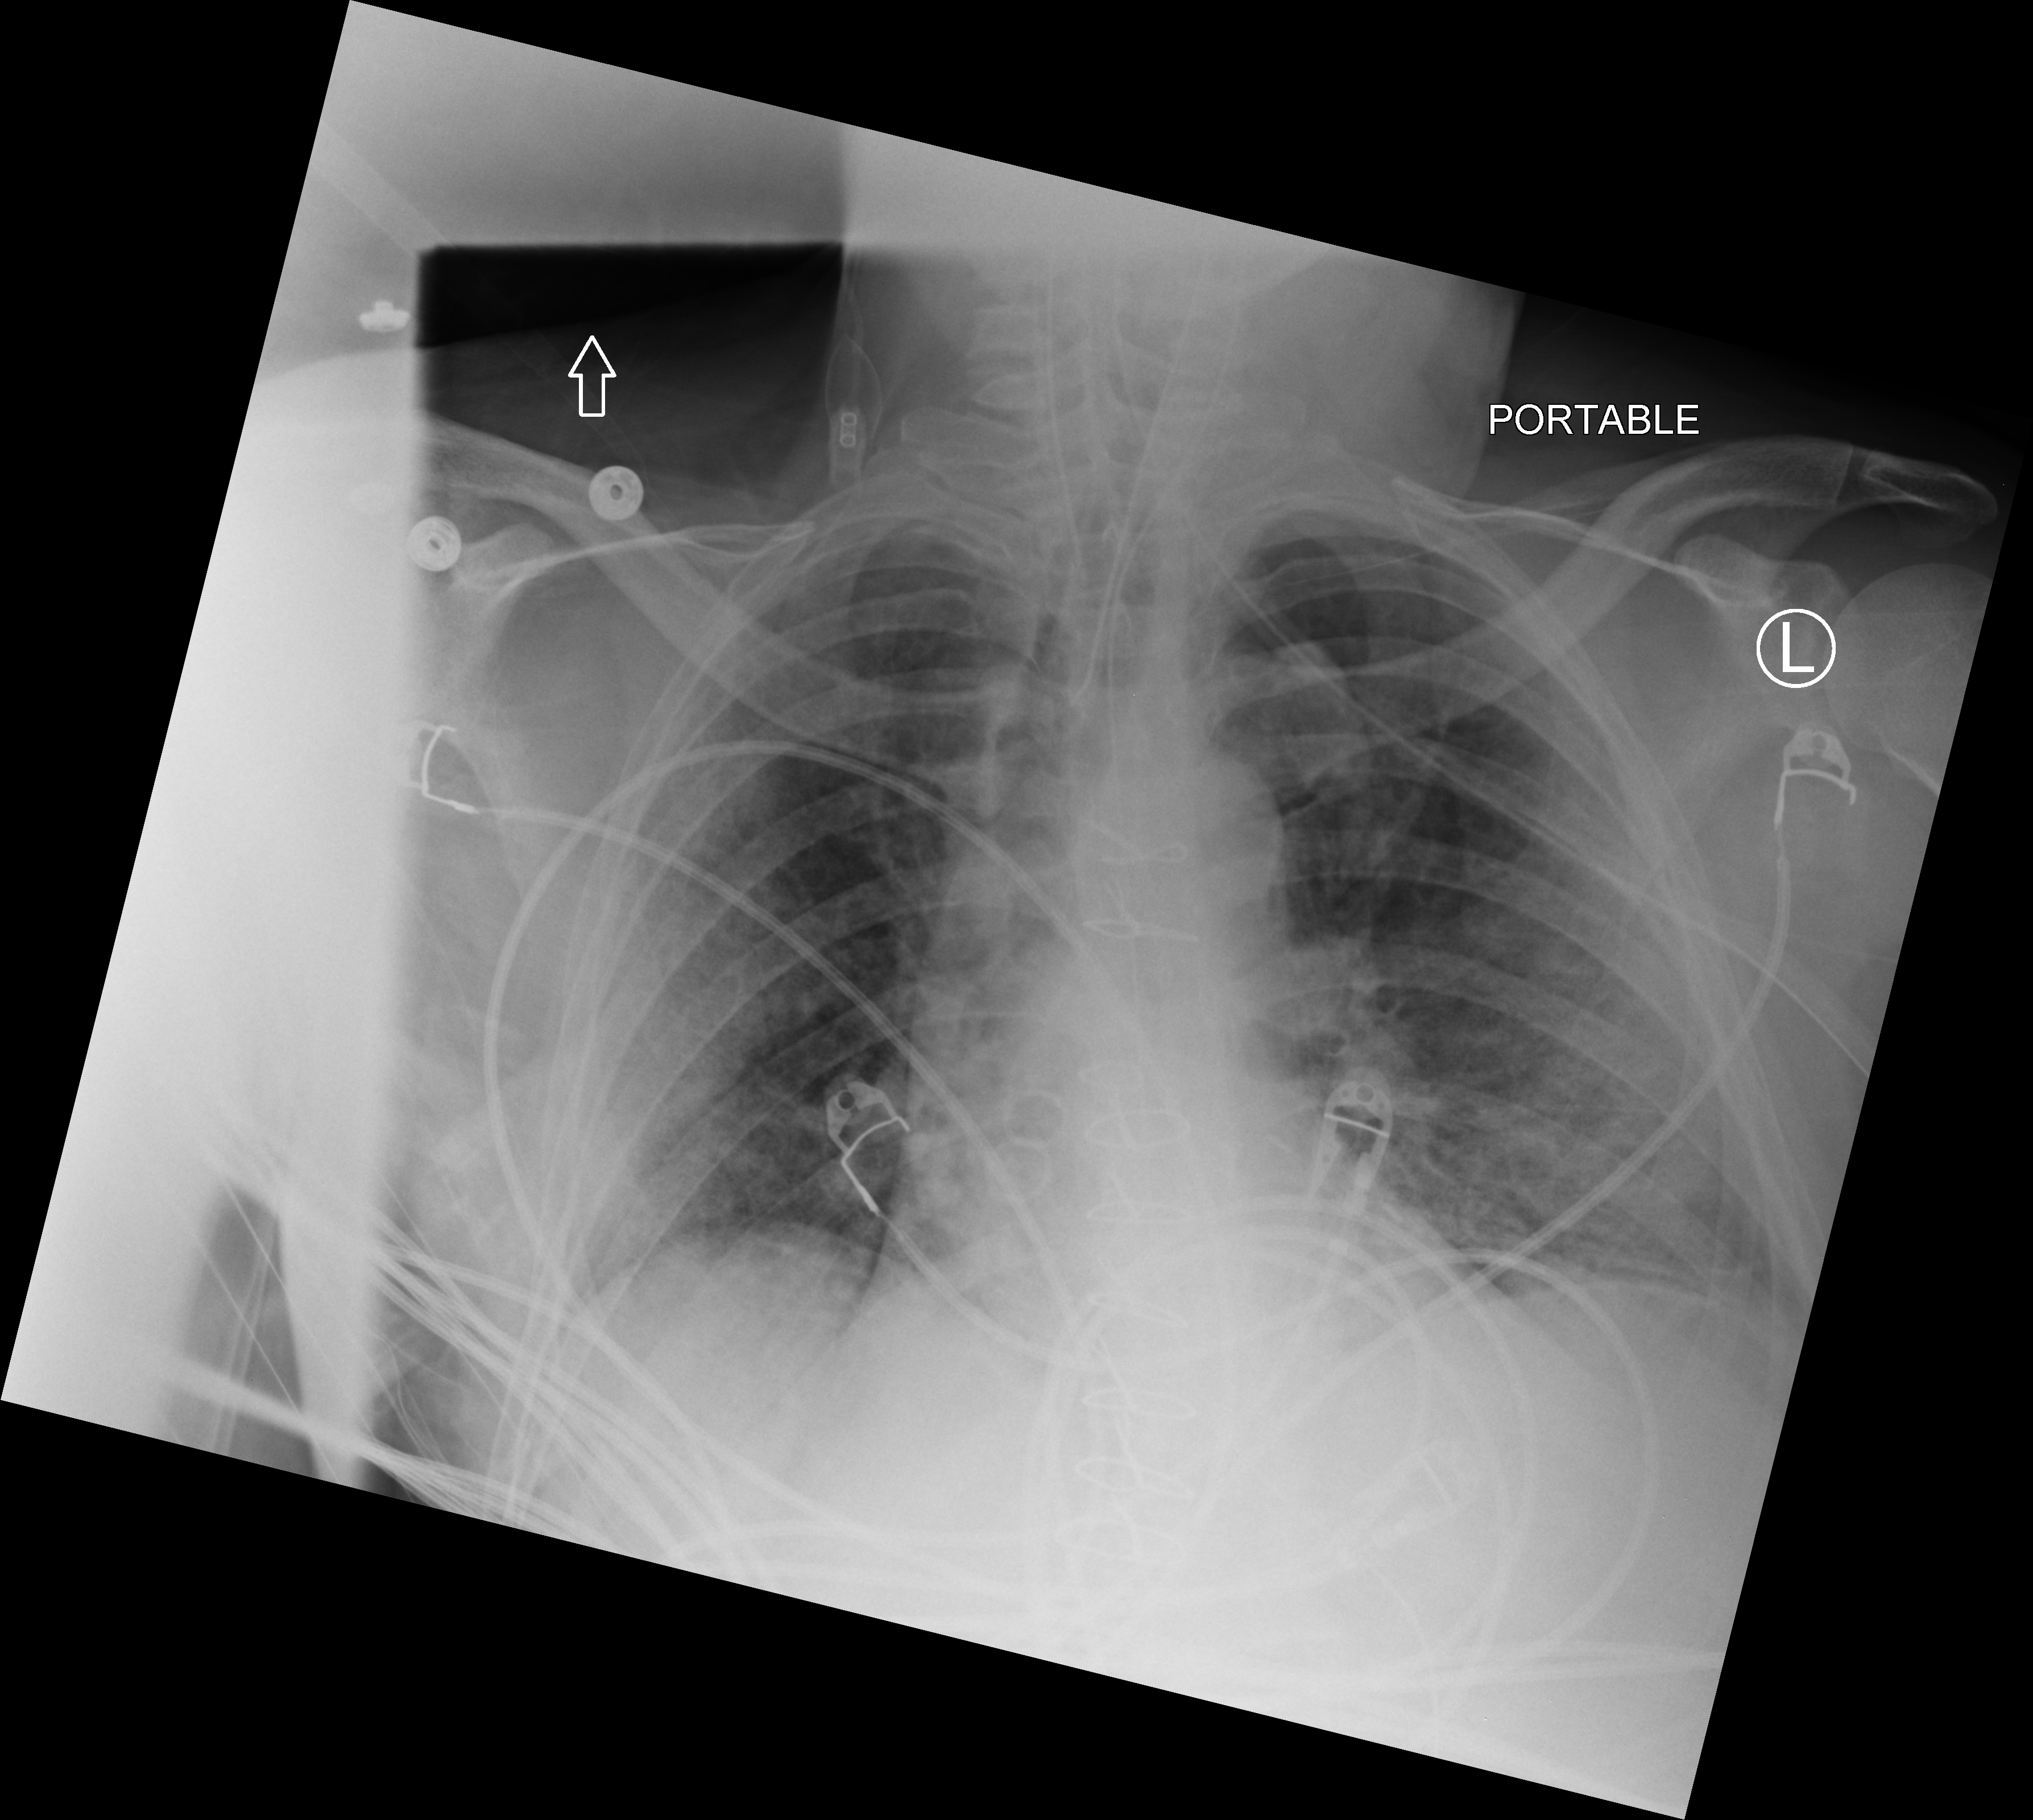
Bedside chest radiograph (computed radiography). Patient hospitalised with COVID-19; male, aged 18–59 years.
Hospital-stay facts (about this admission, not read from this image; timing relative to this image not recorded): admitted to intensive care during this hospital stay: yes.